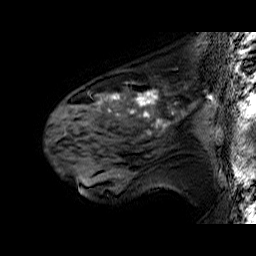
Breast MRI (dynamic contrast-enhanced), one sagittal slice. Position 39 of 60 along the scan axis. Dynamic contrast-enhanced series, time point 2 of 6 at this slice position (early post-contrast). 1.5 T. TE 6.4 ms, TR 32.9 ms. 4 mm slice thickness. 256 × 256 image matrix. Female patient. From the clinical record (not read from this slice): setting: breast cancer imaged before/during neoadjuvant chemotherapy; receptor status: HER2-positive.
Outlined on this slice (semi-automatic segmentation, software-assisted and operator-edited):
- analysis volume of interest (the breast-tissue region the enhancement analysis was run in; not a lesion): box from (x=51, y=78) to (x=196, y=160) px
- tumour enhancement mask (voxels above the 100 % enhancement threshold inside the analysis volume of interest): (x=98, y=90)–(x=162, y=134)